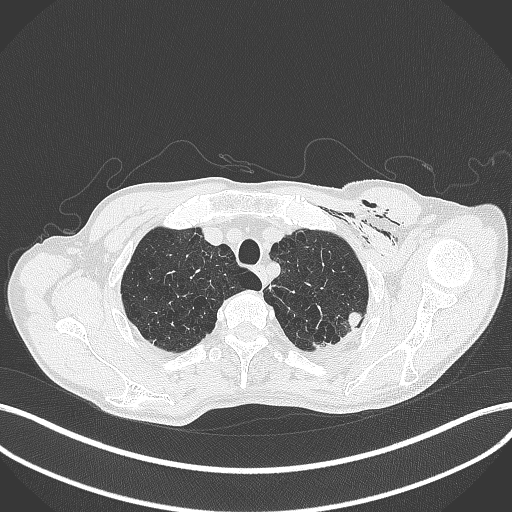
Chest CT, one axial slice; lung window (W 1500 / L -600 HU); 1 mm slice thickness; 512 × 512 image matrix, field of view 400 × 400 mm. Male patient, age 58 years. Case-level facts recorded for this patient, not image findings: clinical TNM (as recorded): T3 N0 M0.
Structures marked on this image (bounding box drawn by a radiologist):
- lung tumour (recorded histology: adenocarcinoma): bounding box [x1, y1, x2, y2] px = [345, 310, 366, 332]